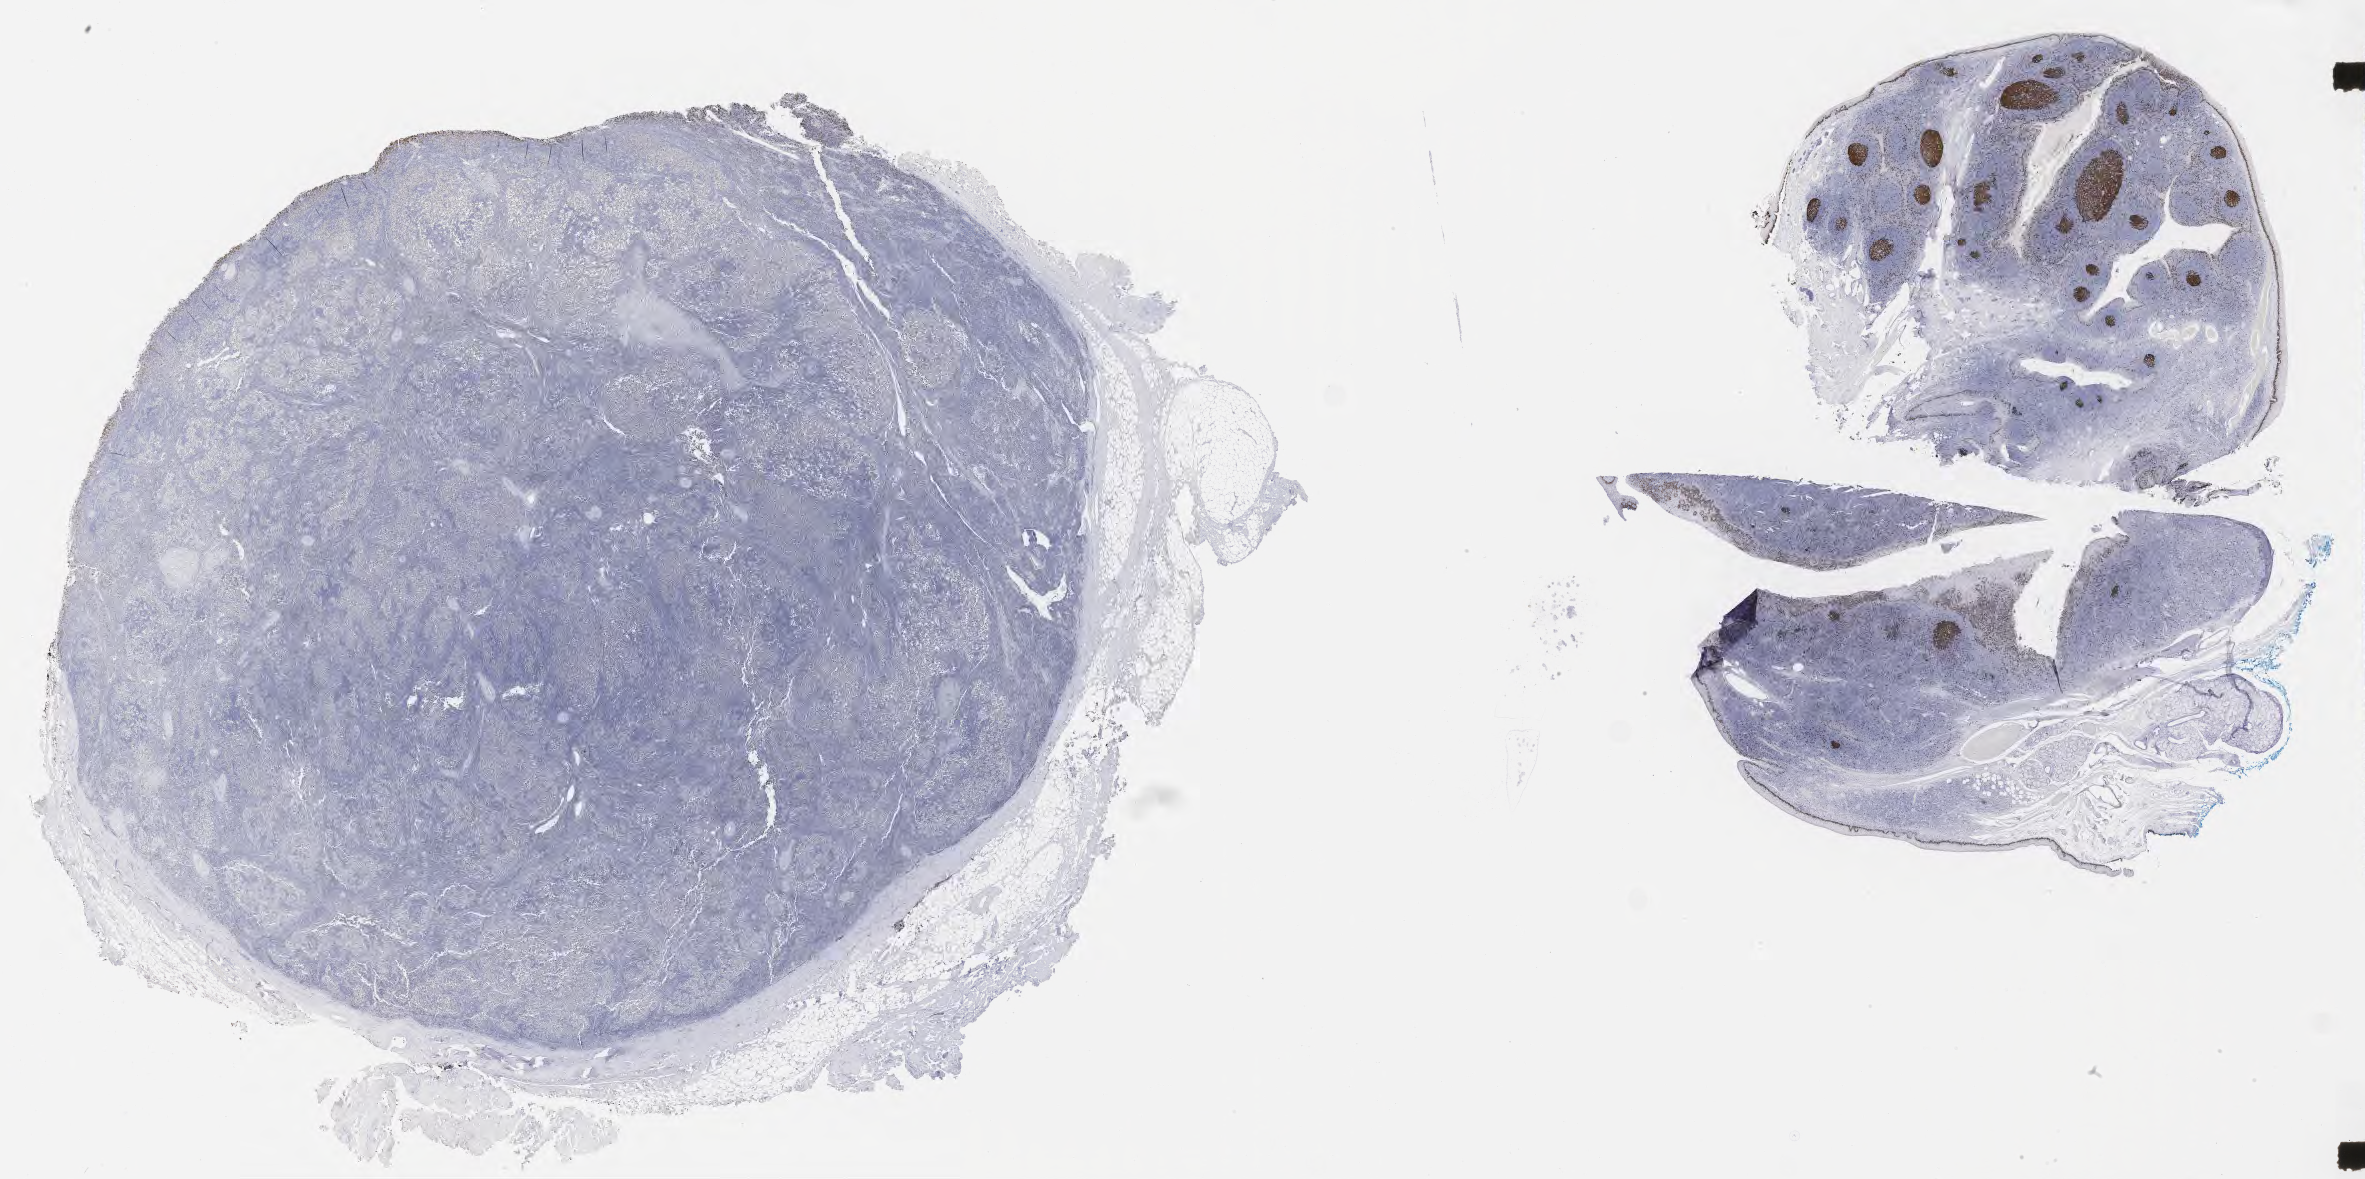
Whole-slide image, immunohistochemical stain for Ki-67, low-resolution overview of the scanned area, about 38.2 x 19.1 mm, tumor tissue, anatomic site: lymph node. Male patient, 46 years old.
Diagnosis: Diffuse large B-cell lymphoma, NOS.